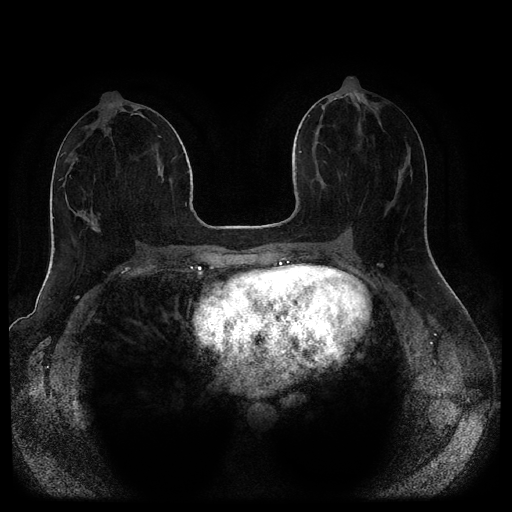
Breast MRI (dynamic contrast-enhanced, multi-phase), one axial slice; slice 44 of 116 in the series (ordered by position); dynamic contrast-enhanced series, time point 2 of 5 at this slice position (early post-contrast); 1.5 T; TE 2.6 ms, TR 5.3 ms; 2 mm slice thickness; 512 × 512 image matrix. Patient: female, 44 years.
Outlined on this slice (semi-automatic segmentation, software-assisted and operator-edited):
- breast lesion (labelled benign in the annotation): bounding box <91,219,103,235> (left, top, right, bottom; pixels)